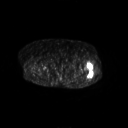
FDG PET of an extremity soft-tissue mass (from a PET/CT study), one axial slice. Slice 254 of 267 in the series (ordered by position). 128 × 128 image matrix, field of view 700 × 700 mm. Female patient, age 62 years. Case-level facts recorded for this patient, not image findings: histological type: undifferentiated – high grade; grade: high; site of the primary tumour: left thigh.
Outlined on this slice (expert contour drawn on MRI and transferred to this co-registered scan by the dataset authors):
- gross tumour volume including surrounding oedema: bounding box <86,64,94,78> (left, top, right, bottom; pixels)
- gross tumour volume (mass): <87,64,94,78>